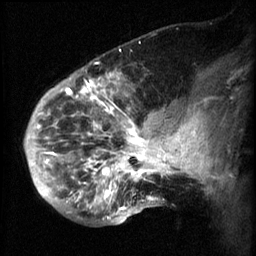
Breast MRI (dynamic contrast-enhanced), one sagittal slice; position 20 of 60 along the scan axis; 3 images stored at this slice position (order not interpretable as contrast timing); 1.5 T; TE 4.2 ms, TR 8.2 ms; 2.3 mm slice thickness; 256 × 256 image matrix, field of view 200 × 200 mm. Female patient, age 50 years.
Structures marked on this image (semi-automatically segmented with operator editing):
- analysis volume of interest (the breast-tissue region the enhancement analysis was run in; not a lesion): box from (x=50, y=64) to (x=169, y=217) px
- tumour enhancement mask (voxels above the 70 % enhancement threshold inside the analysis volume of interest): (x=50, y=74)–(x=169, y=211)